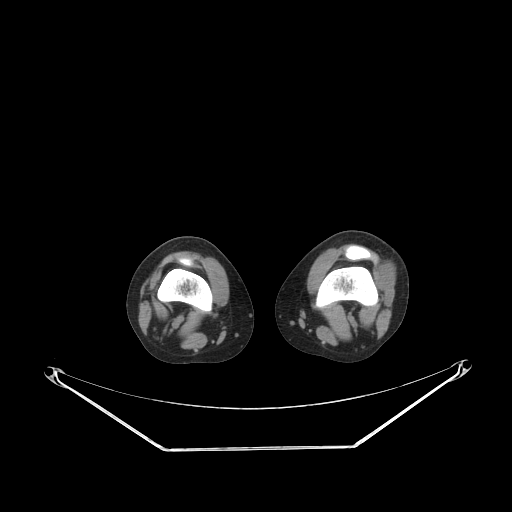
CT of an extremity soft-tissue mass (from a PET/CT study), one axial slice. Position 168 of 223 along the scan axis. Reconstruction kernel STANDARD. Soft-tissue window (W 400 / L 40 HU). 3.75 mm slice thickness. 512 × 512 image matrix, field of view 500 × 500 mm. Female patient. From the clinical record (not read from this slice): histological type: spindle cell suggestive of biphasic synovial sarcoma; grade: intermediate; site of the primary tumour: left knee.
Annotated regions visible in this slice (expert contour drawn on MRI and transferred to this co-registered scan by the dataset authors):
- gross tumour volume including surrounding oedema: bounding box (x1, y1, x2, y2) in pixels: (374, 265, 394, 305)
- gross tumour volume (mass): (374, 269, 394, 305)